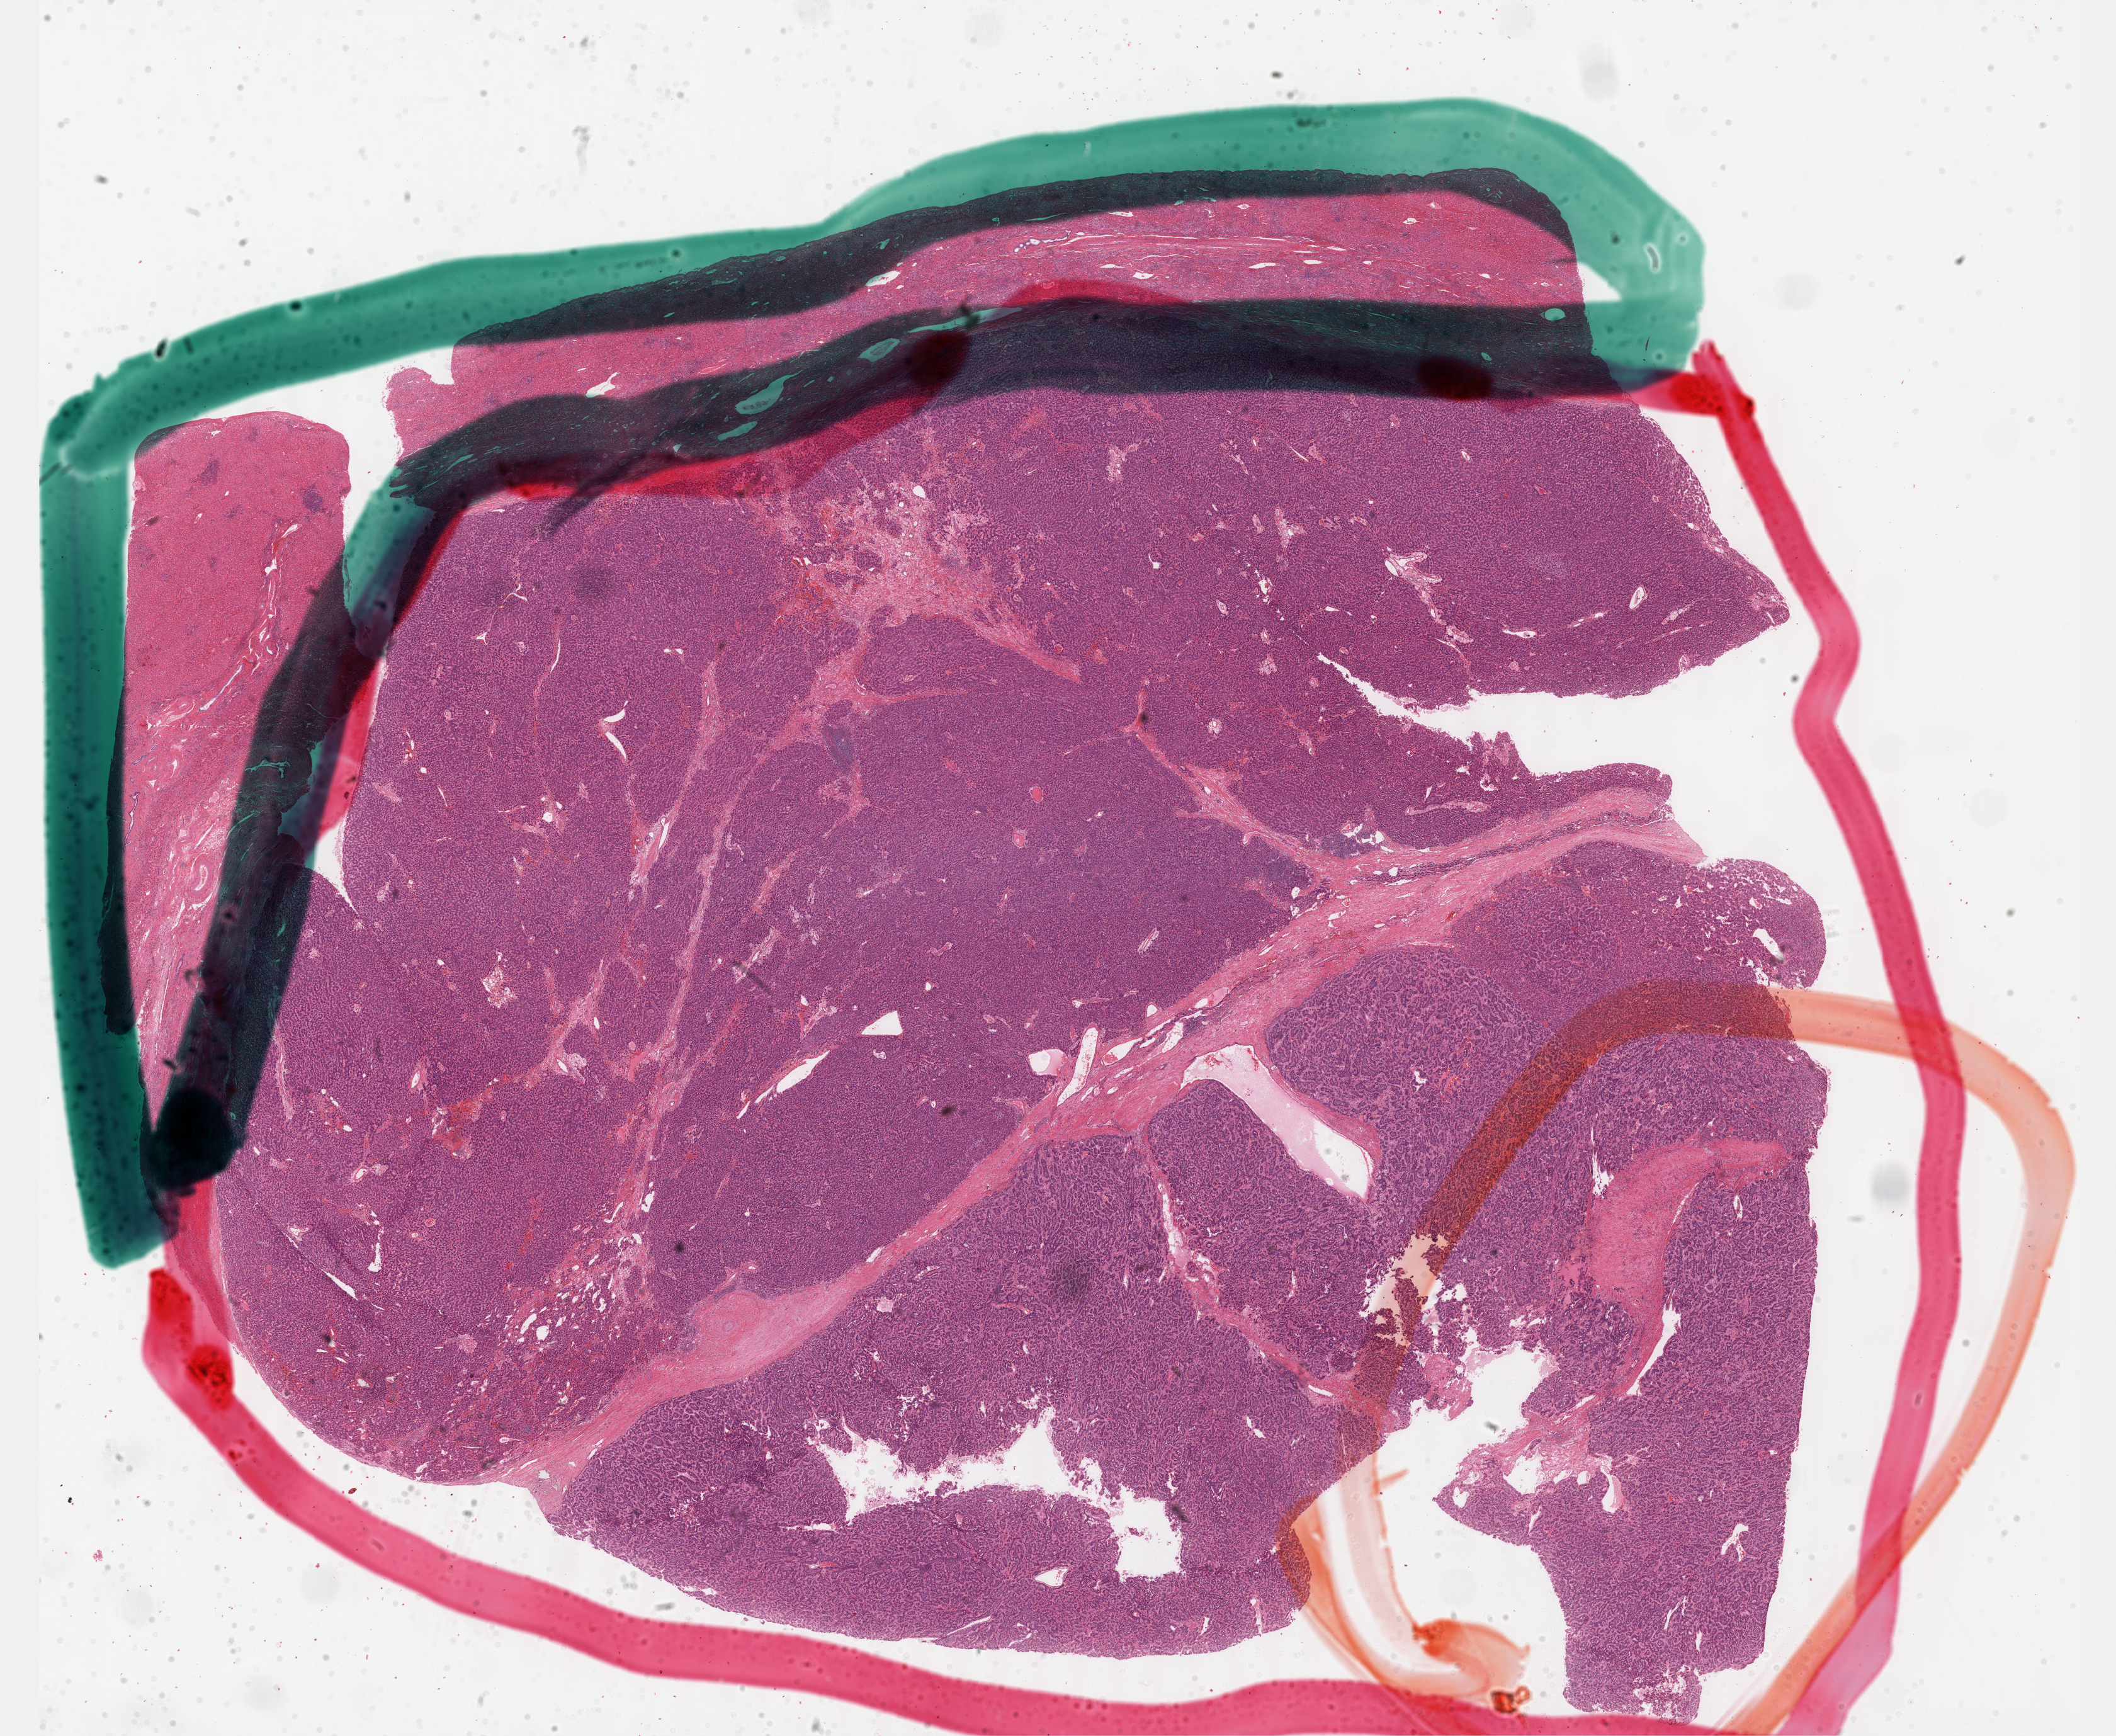
Whole-slide histology image, Hematoxylin and eosin (H&E) stained — low-resolution overview of the scanned area, about 27.2 x 22.3 mm, FFPE section, sample: primary tumour, liver. Female patient; age at initial diagnosis 59 years. Histologic grade: G3 (poorly differentiated).
* AJCC pathologic stage: IIIA (7th edition)
* histologic diagnosis: Hepatocellular carcinoma, NOS